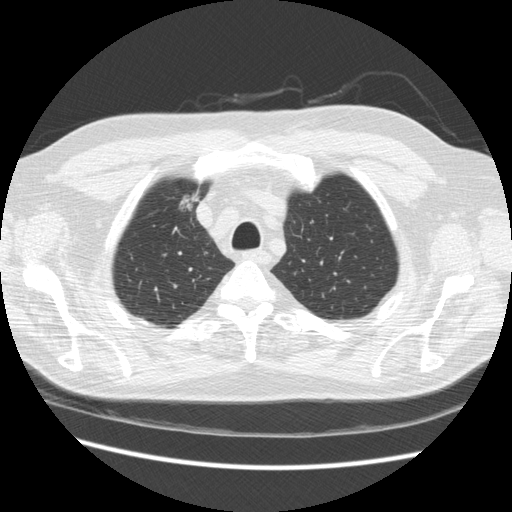
Low-dose screening chest CT, one axial slice. Position 190 of 234 along the scan axis. Reconstruction kernel STANDARD. Lung window (W 1500 / L -600 HU). 2.5 mm slice thickness. 512 × 512 image matrix, field of view 360 × 360 mm.
Annotated regions visible in this slice (outlined manually by an expert reader):
- lesion 1 (tumor, upper lobe of right lung): bounding box [x1, y1, x2, y2] px = [179, 191, 199, 212]